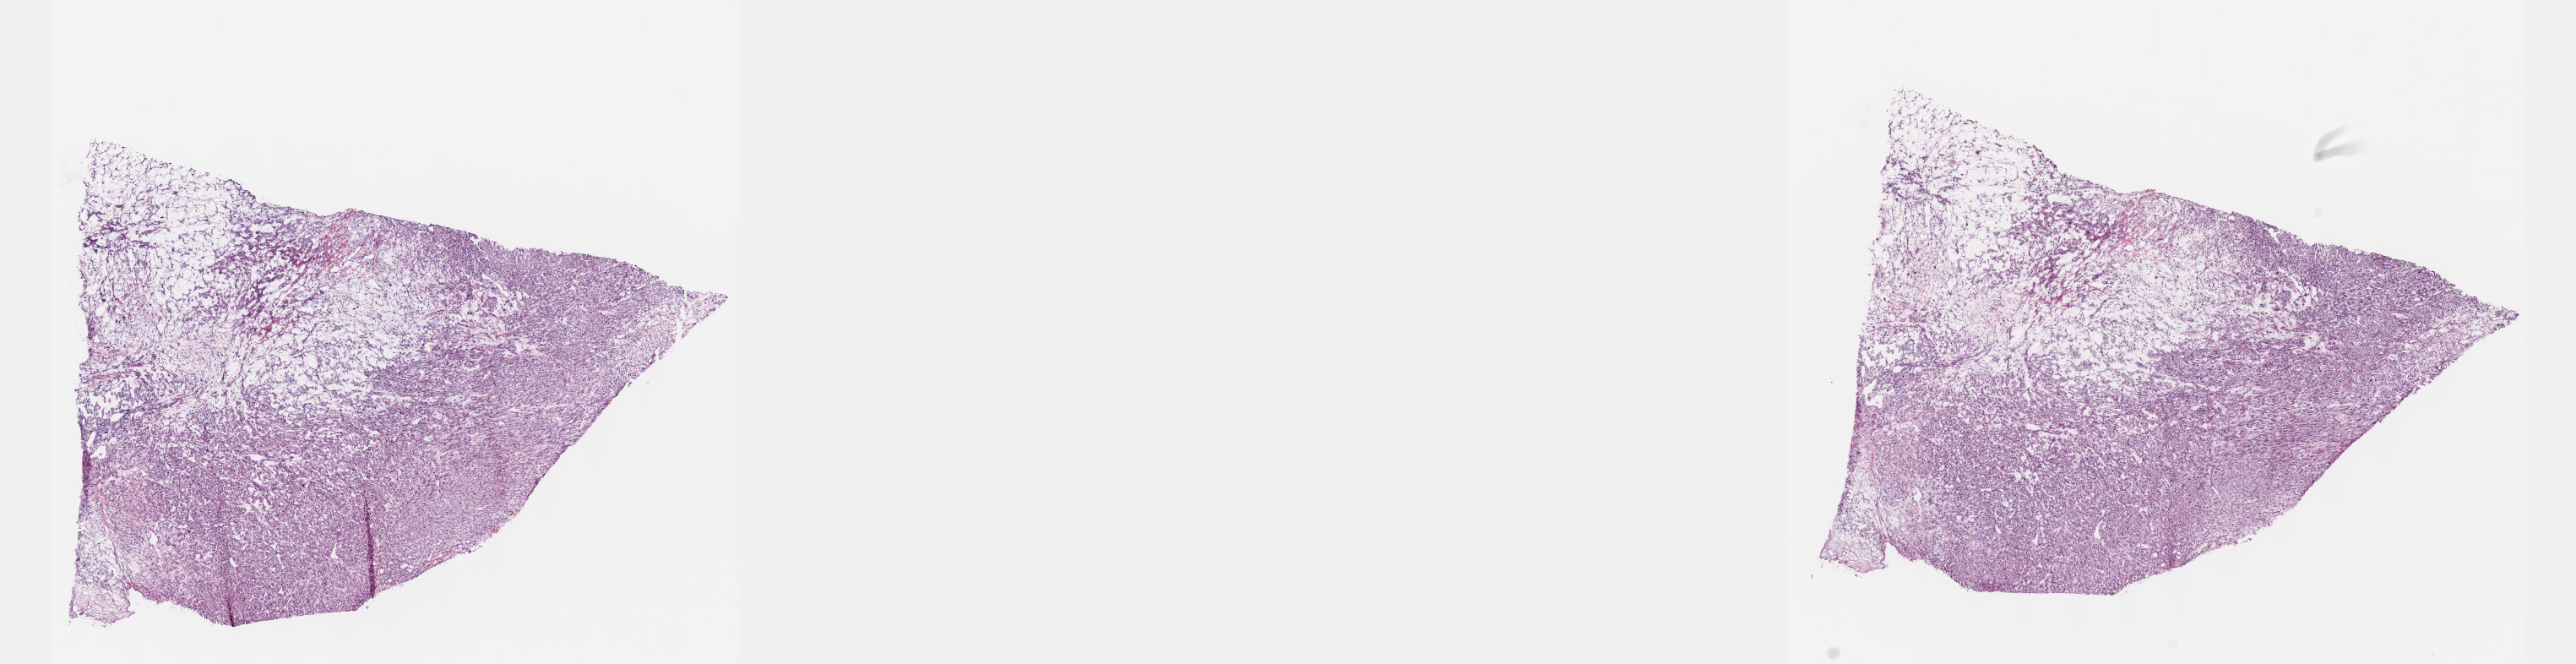
Whole-slide histology image, H&E — low-resolution overview of the scanned area, about 24.6 x 6.4 mm. Frozen section from the top of the tissue portion. Connective, subcutaneous and other soft tissues, primary tumour sample. Female, age 63 years at initial diagnosis. Pathologist review of this section (percent, as recorded): tumour cells 95%, tumour nuclei 80%, normal cells 0%, stromal cells 0%, necrosis 5%. Infiltration values recorded for this section: lymphocyte infiltration 3%, monocyte infiltration 0%, neutrophil infiltration 0%.
• pathologic diagnosis: Leiomyosarcoma, NOS (connective, subcutaneous and other soft tissues of lower limb and hip)